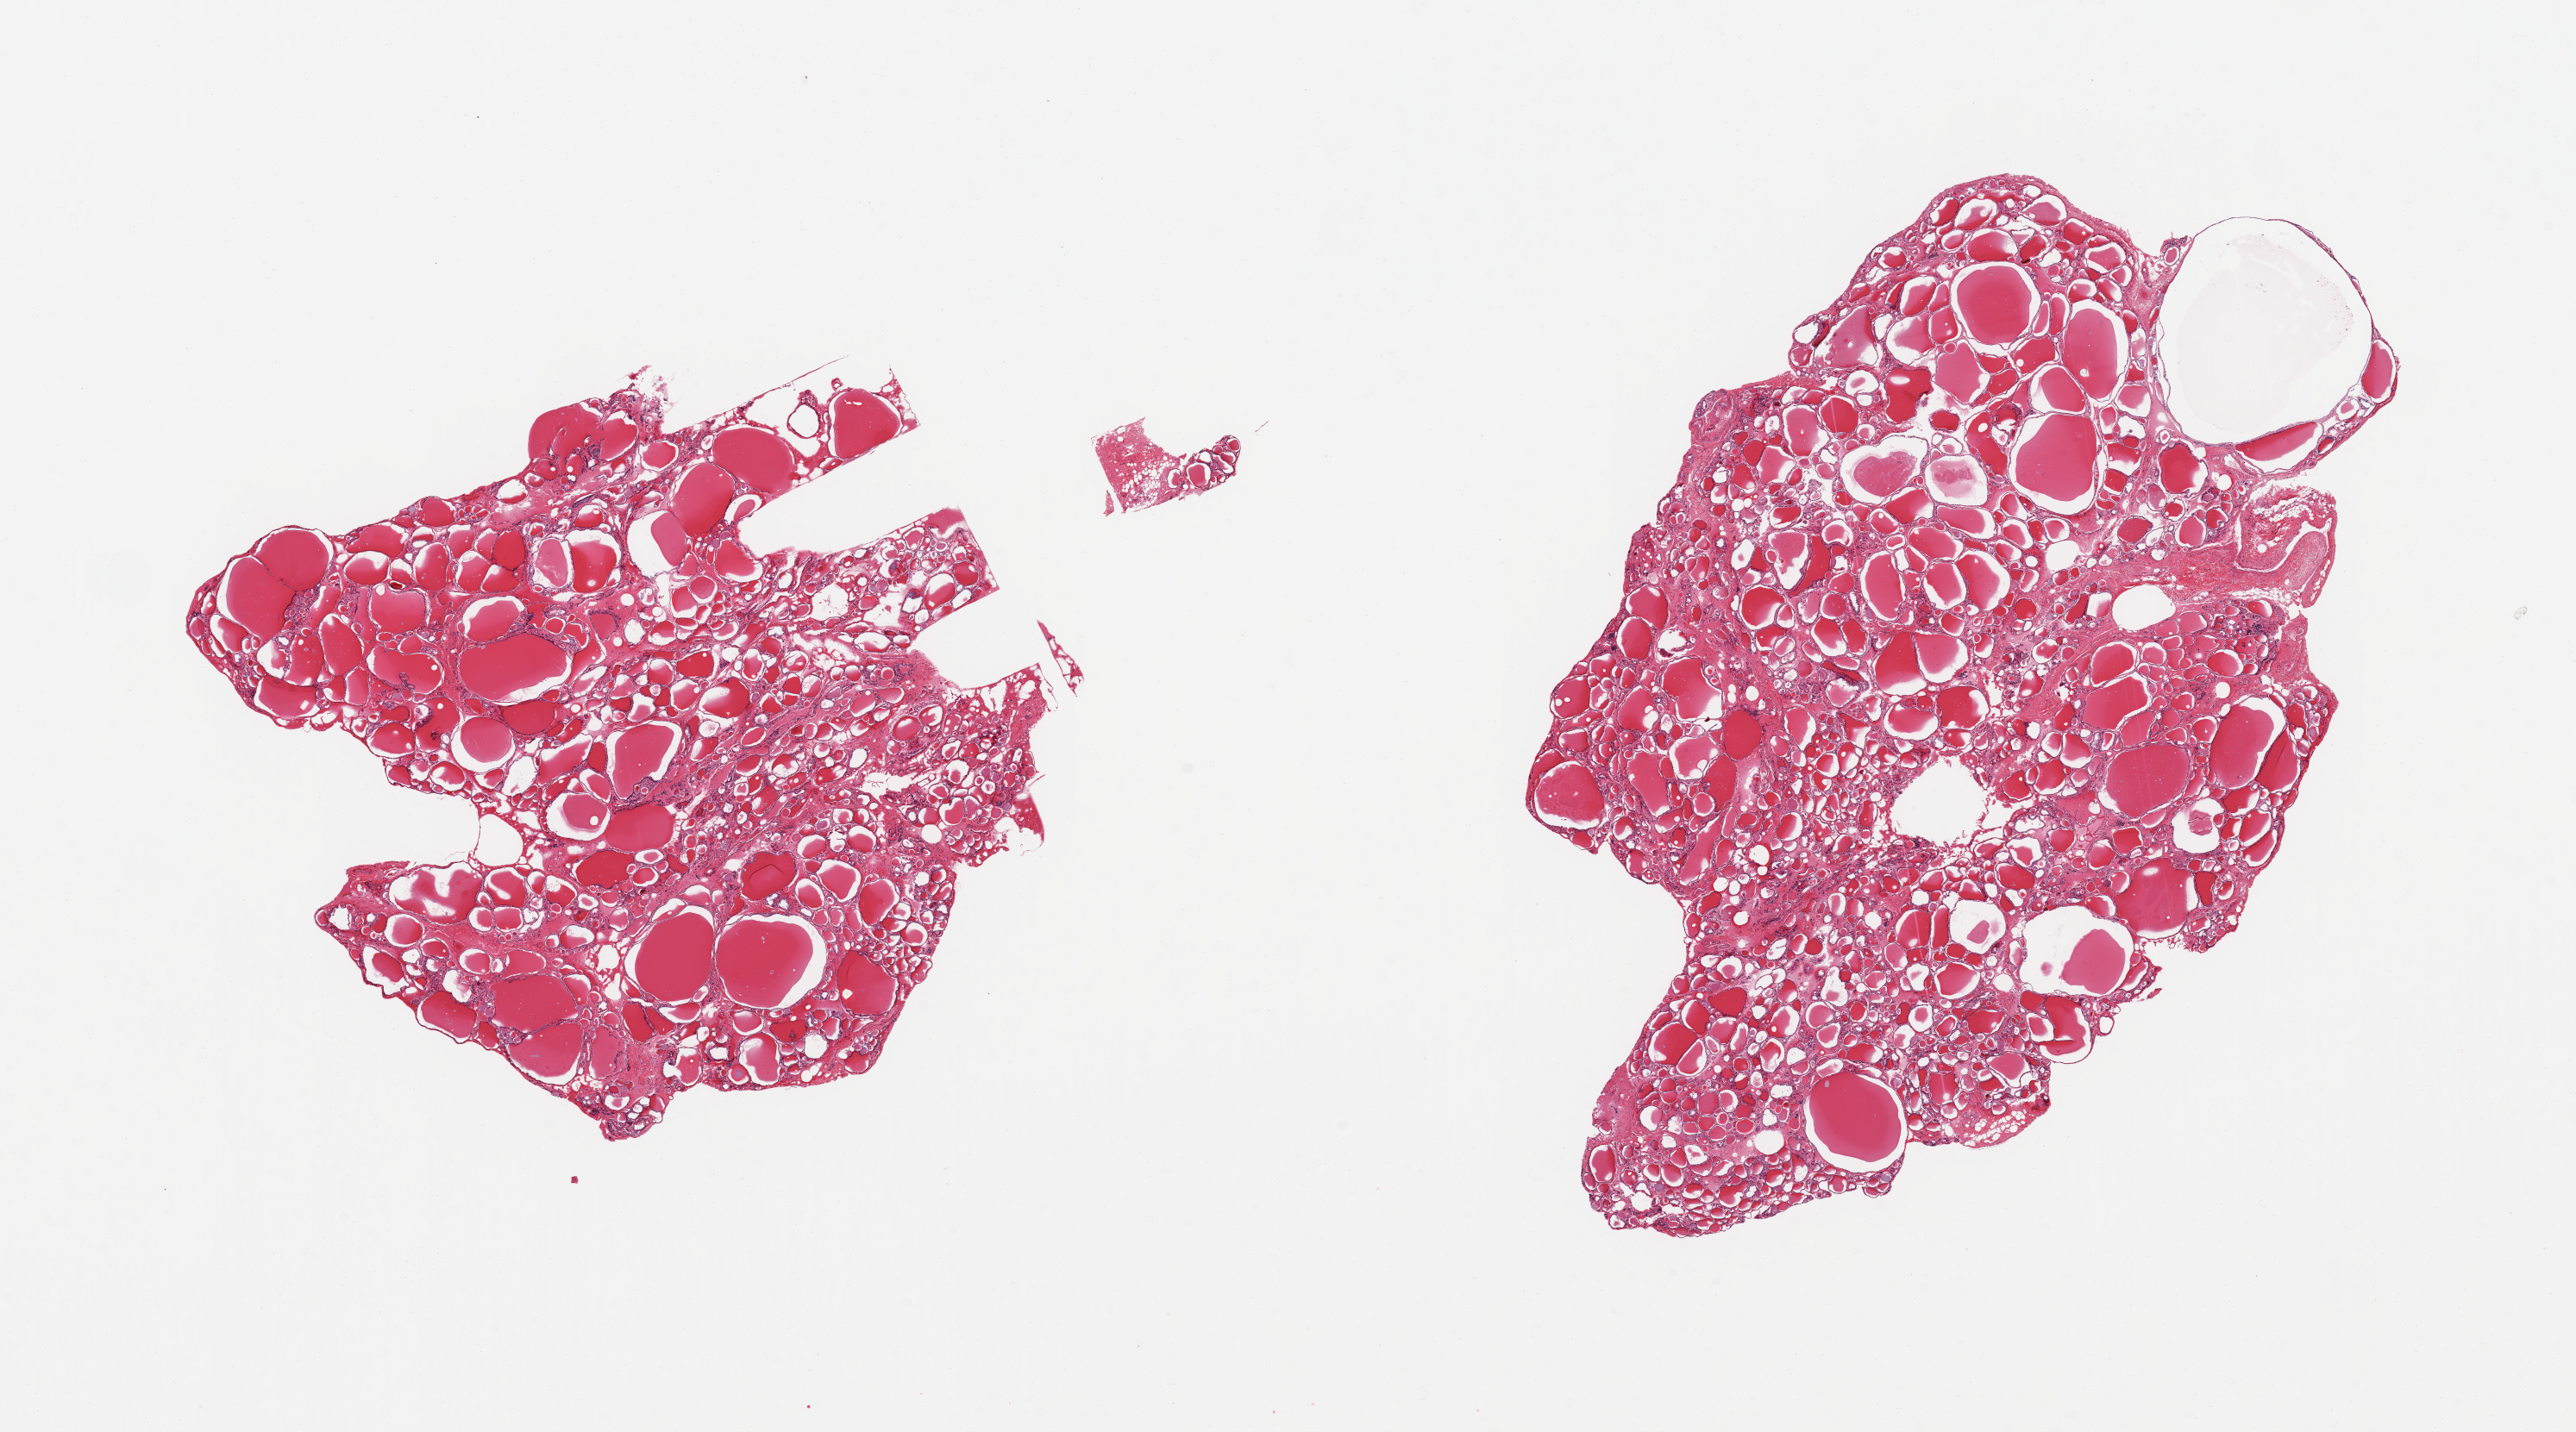
Hematoxylin and eosin (H&E) whole-slide image — low-resolution overview of the scanned area, about 23.6 x 13.1 mm (slide scanned at 20x), PAXgene-fixed paraffin-embedded (PFPE) section, target tissue: thyroid, tissue donor sample.
Pathologist's review note for this sample: 2 pieces; variably sized follicles.